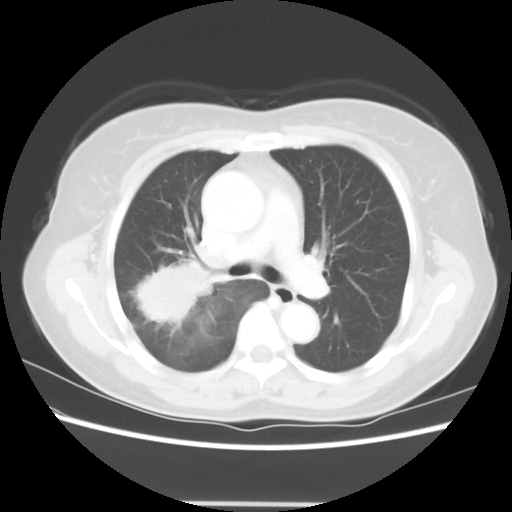
Chest CT, one axial slice; slice 37 of 56 in the series (ordered by position); reconstruction kernel STANDARD; 120 kVp; lung window (W 1500 / L -600 HU); 512 × 512 image matrix. Female patient, age 55 years. From the clinical record (not read from this slice): clinical TNM (as recorded): T2 N1 M0; histopathological grade: G2-3.
Structures marked on this image (bounding box drawn by a radiologist):
- lung tumour (recorded histology: adenocarcinoma): bounding box [x1, y1, x2, y2] px = [128, 249, 219, 342]